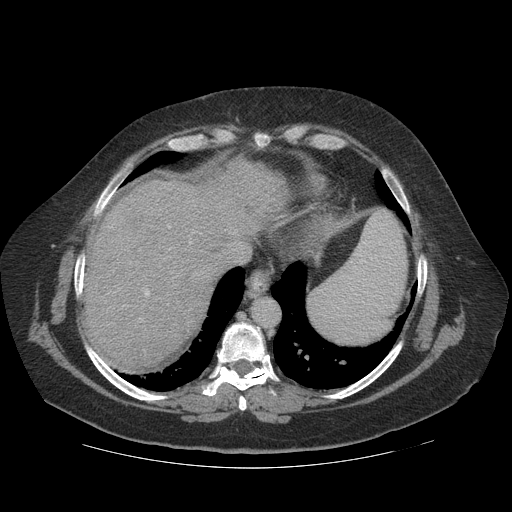
Contrast-enhanced abdominal CT (liver protocol), one axial slice; position 98 of 121 along the scan axis; 140 kVp; soft-tissue window (W 400 / L 40 HU); 2.5 mm slice thickness; 512 × 512 image matrix, field of view 420 × 420 mm. From the clinical record (not read from this slice): diagnosis: hepatocellular carcinoma (patient treated with transarterial chemoembolisation; whether this scan precedes or follows treatment is not stated here); TNM stage (as recorded): Stage-IIIA; Child-Pugh class: A; tumour differentiation: well differentiated.
Outlined on this slice (semi-automatic segmentation, software-assisted and operator-edited):
- abdominal aorta: bounding box <254,299,280,327> (left, top, right, bottom; pixels)
- liver parenchyma outside the tumour (the mass and vessels are separate outlines, so this box may not span the whole liver): <82,160,286,372>
- liver vessels: <109,224,236,321>